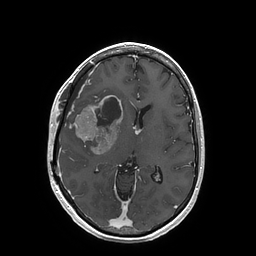
Brain MRI from a brain-tumour surgery series, one axial slice. T1-weighted post-contrast. 1 mm slice thickness. 256 × 256 image matrix, field of view 250 × 250 mm. From the clinical record (not read from this slice): histopathology: Glioblastoma; WHO grade: 4; IDH mutation: no; tumour location: Right Insular.
Outlined on this slice (manually delineated by an expert):
- tumour: bounding box <73,95,123,155> (left, top, right, bottom; pixels)